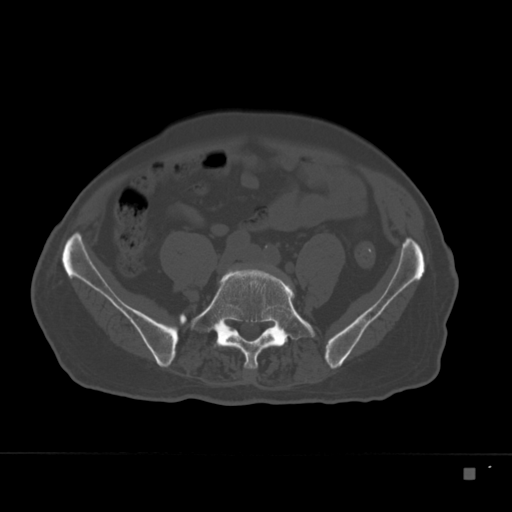
CT including the spine, one axial slice. Position 24 of 332 along the scan axis. Reconstruction kernel Br40s. 120 kVp. Bone window (W 1800 / L 400 HU). 512 × 512 image matrix. Patient: male, 72 years. Case-level facts recorded for this patient, not image findings: primary cancer: skeletal.
Structures marked on this image (semi-automatic segmentation, software-assisted and operator-edited):
- L5 vertebra: box from (x=192, y=269) to (x=315, y=369) px